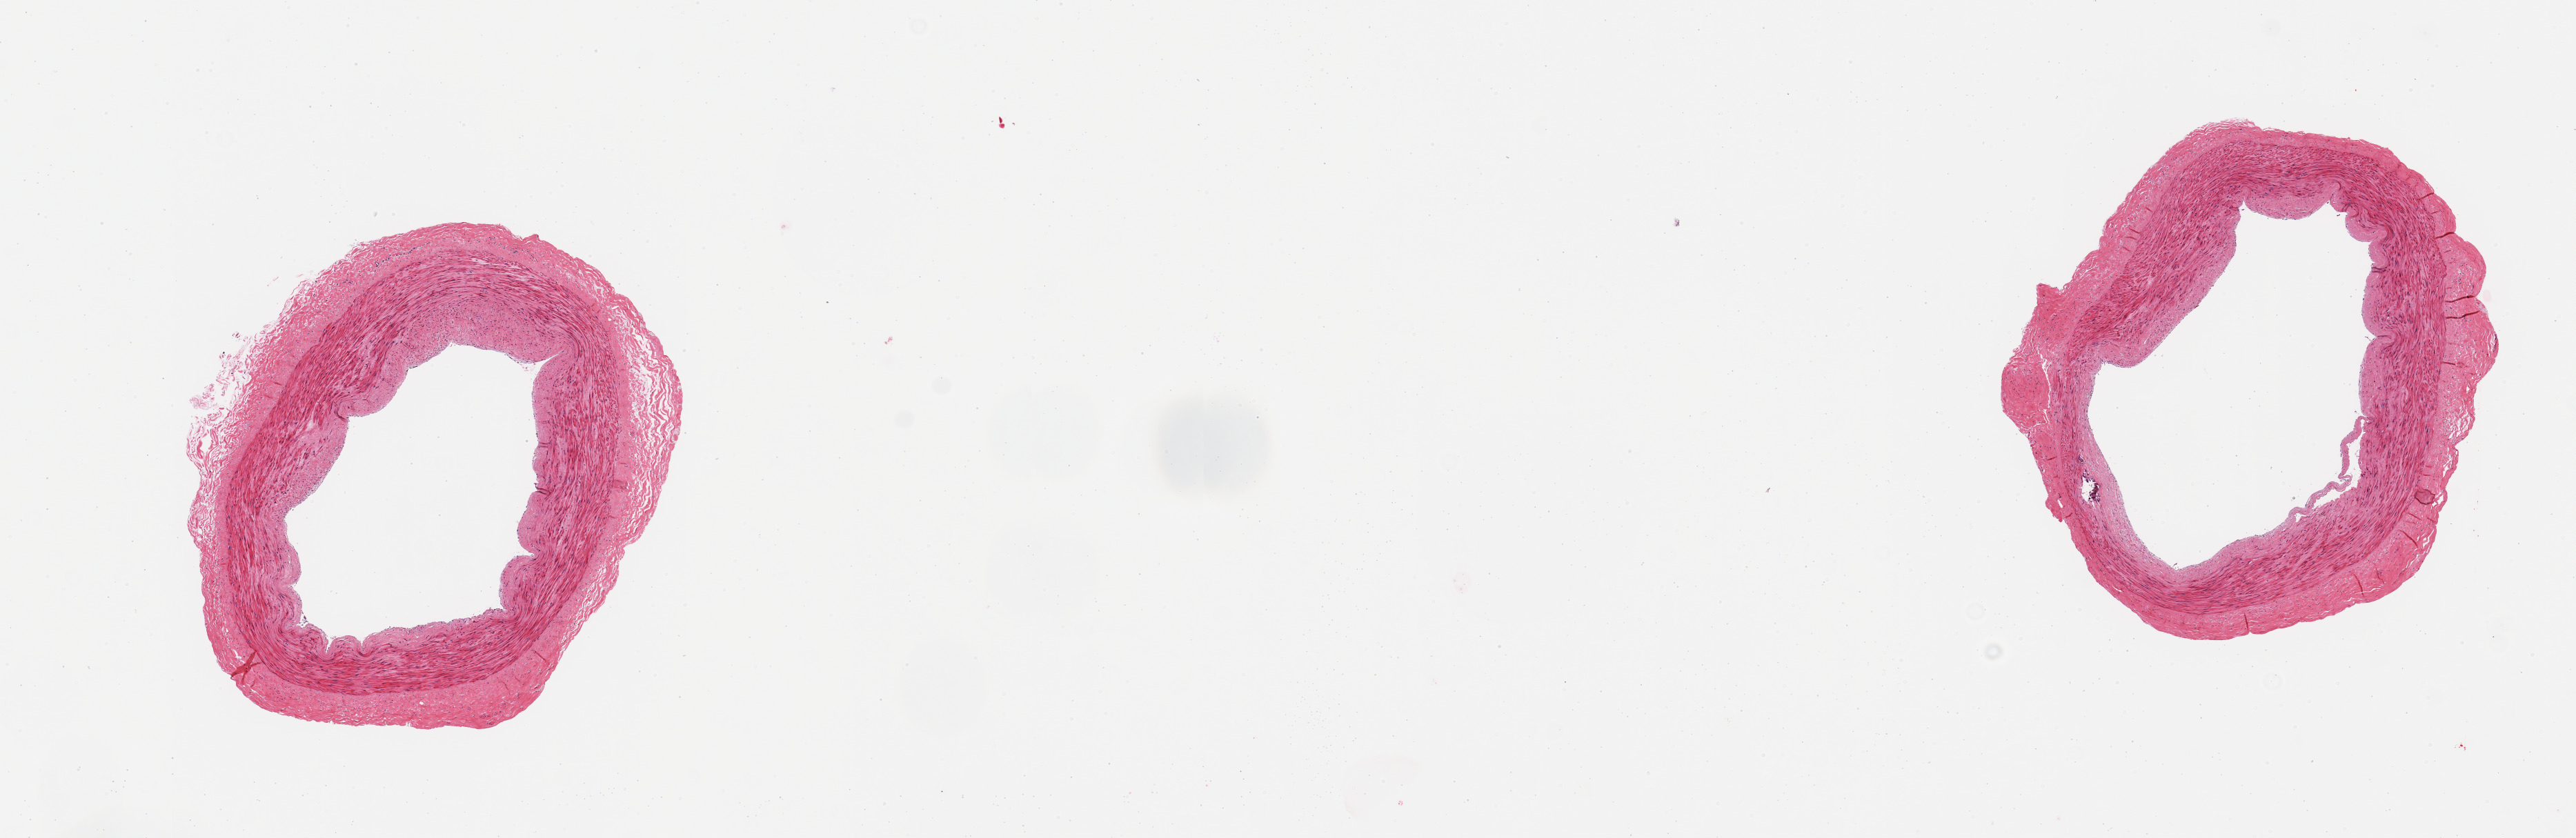
Hematoxylin and eosin (H&E) whole-slide image, a low-resolution overview of the entire scanned area, about 14.8 x 4.8 mm (from a 20x scan); PAXgene-fixed paraffin-embedded (PFPE) section; sampled site (target tissue): tibial artery; donor tissue sample. Donor sex: male.
Pathologist's review note for this sample: 2 pieces; well trimmed, intimal thickening/mild plaque, focus of medial calcification.